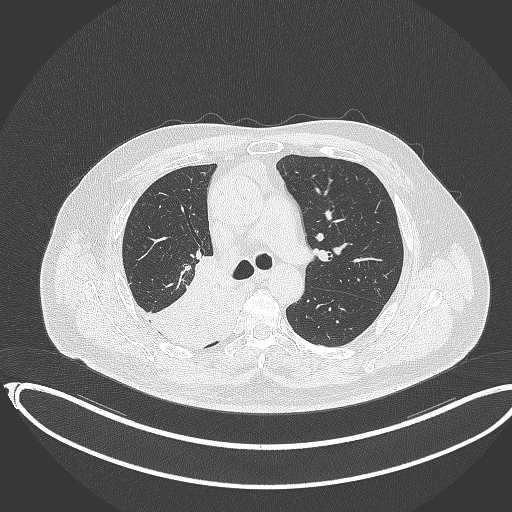
Chest CT, one axial slice. Slice 234 of 403 in the series (ordered by position). Reconstruction kernel B70f. Lung window (W 1500 / L -600 HU). 1 mm slice thickness. 512 × 512 image matrix, field of view 436 × 436 mm. Patient: male, 68 years. Case-level facts recorded for this patient, not image findings: clinical TNM (as recorded): T2a N0 M0.
Structures marked on this image (rectangle marked by the reading radiologist):
- lung tumour (recorded histology: adenocarcinoma): bounding box [x1, y1, x2, y2] px = [142, 257, 228, 344]